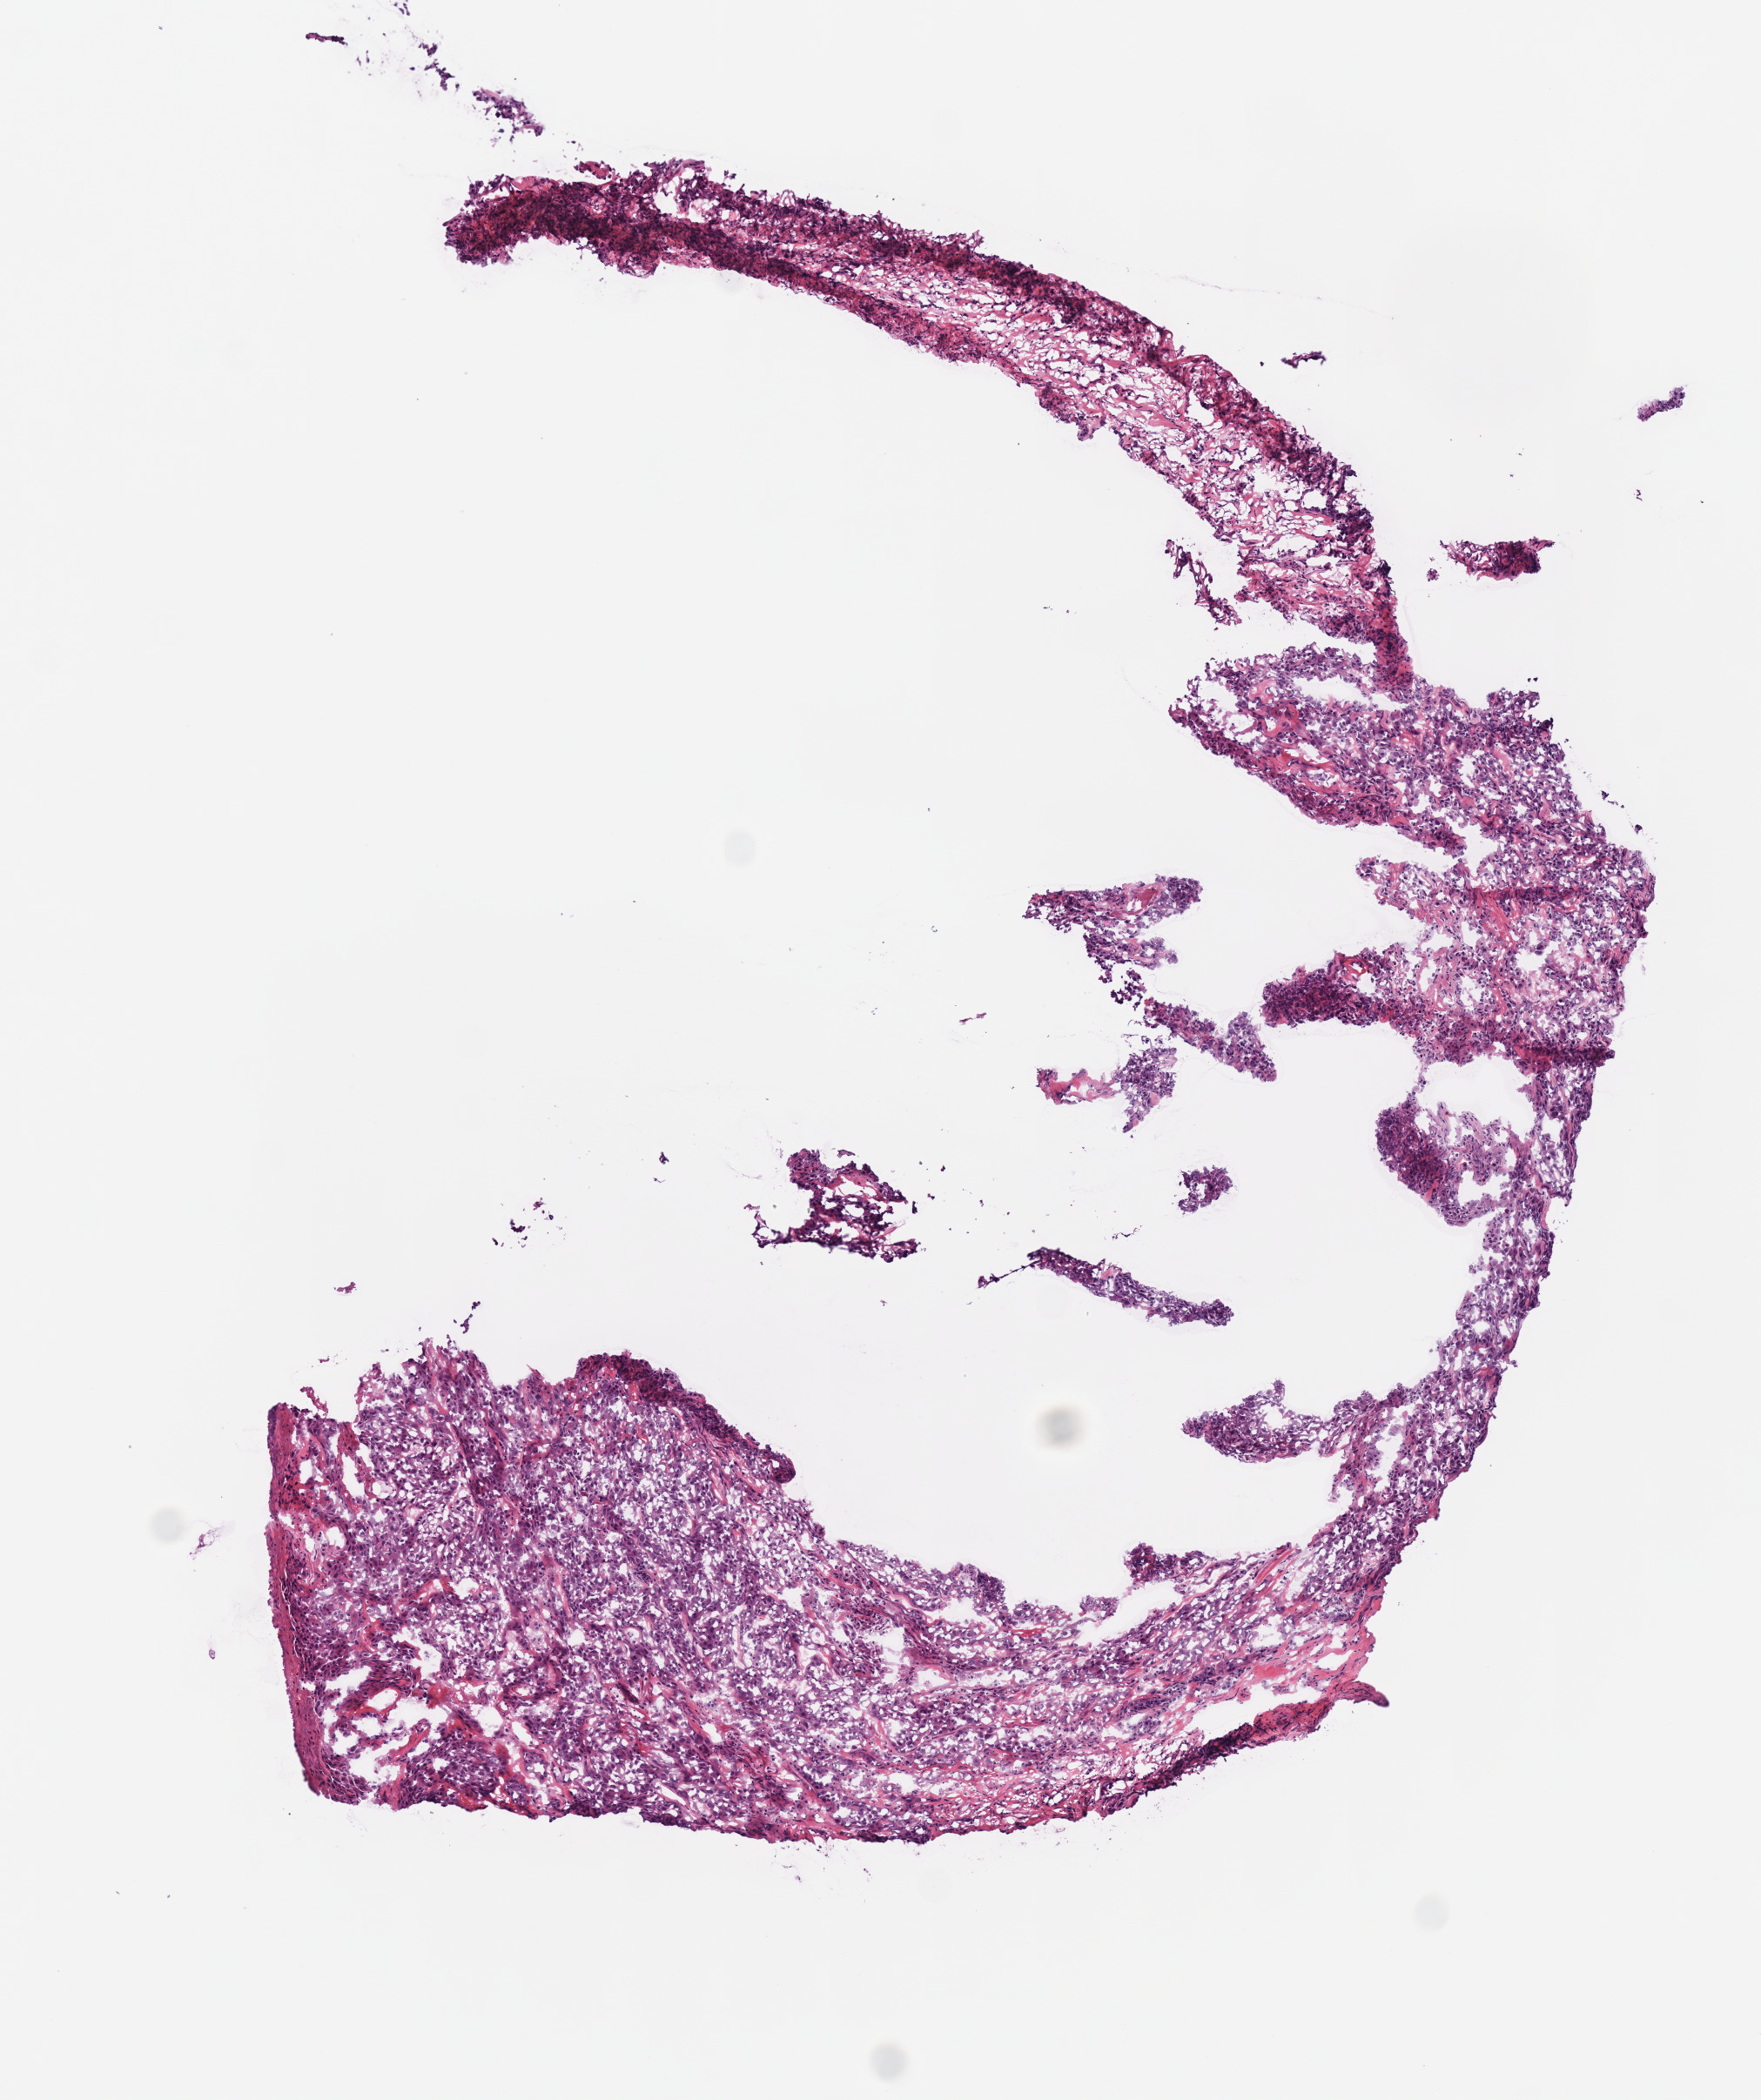
Whole-slide histology image, H&E-stained — whole scanned area (about 4.0 x 4.8 mm, slide scanned at 40x) shown as a low-resolution overview. Frozen section. Head and neck, primary tumour sample. Male patient; age at initial diagnosis 38 years. Histologic grade: GX (grade cannot be assessed). Slide review estimates, as recorded: tumour cells 90%, tumour nuclei 80%, normal cells 0%, stromal cells 10%, necrosis 0%.
Laterality: midline. Diagnosis: Squamous cell carcinoma, NOS (larynx, NOS). AJCC pathologic stage: II.